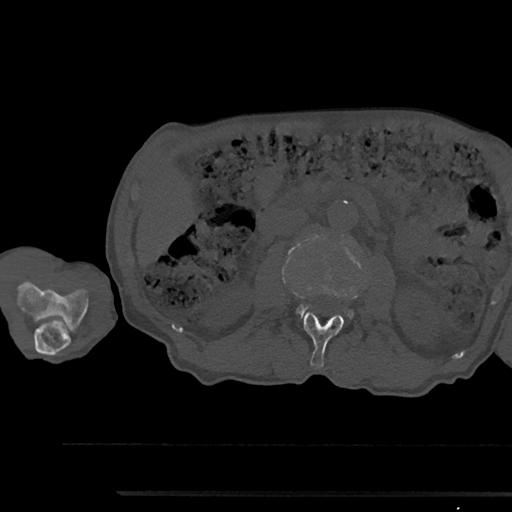
CT including the spine, one axial slice; position 534 of 797 along the scan axis; 120 kVp; bone window (W 1800 / L 400 HU); 0.5 mm slice thickness; 512 × 512 image matrix, field of view 367 × 367 mm. Patient: male, 79 years. Case-level facts recorded for this patient, not image findings: primary cancer: prostate.
Structures marked on this image (semi-automatically segmented with operator editing):
- L2 vertebra: bounding box <303,312,344,367> (left, top, right, bottom; pixels)
- L3 vertebra: <297,306,354,318>